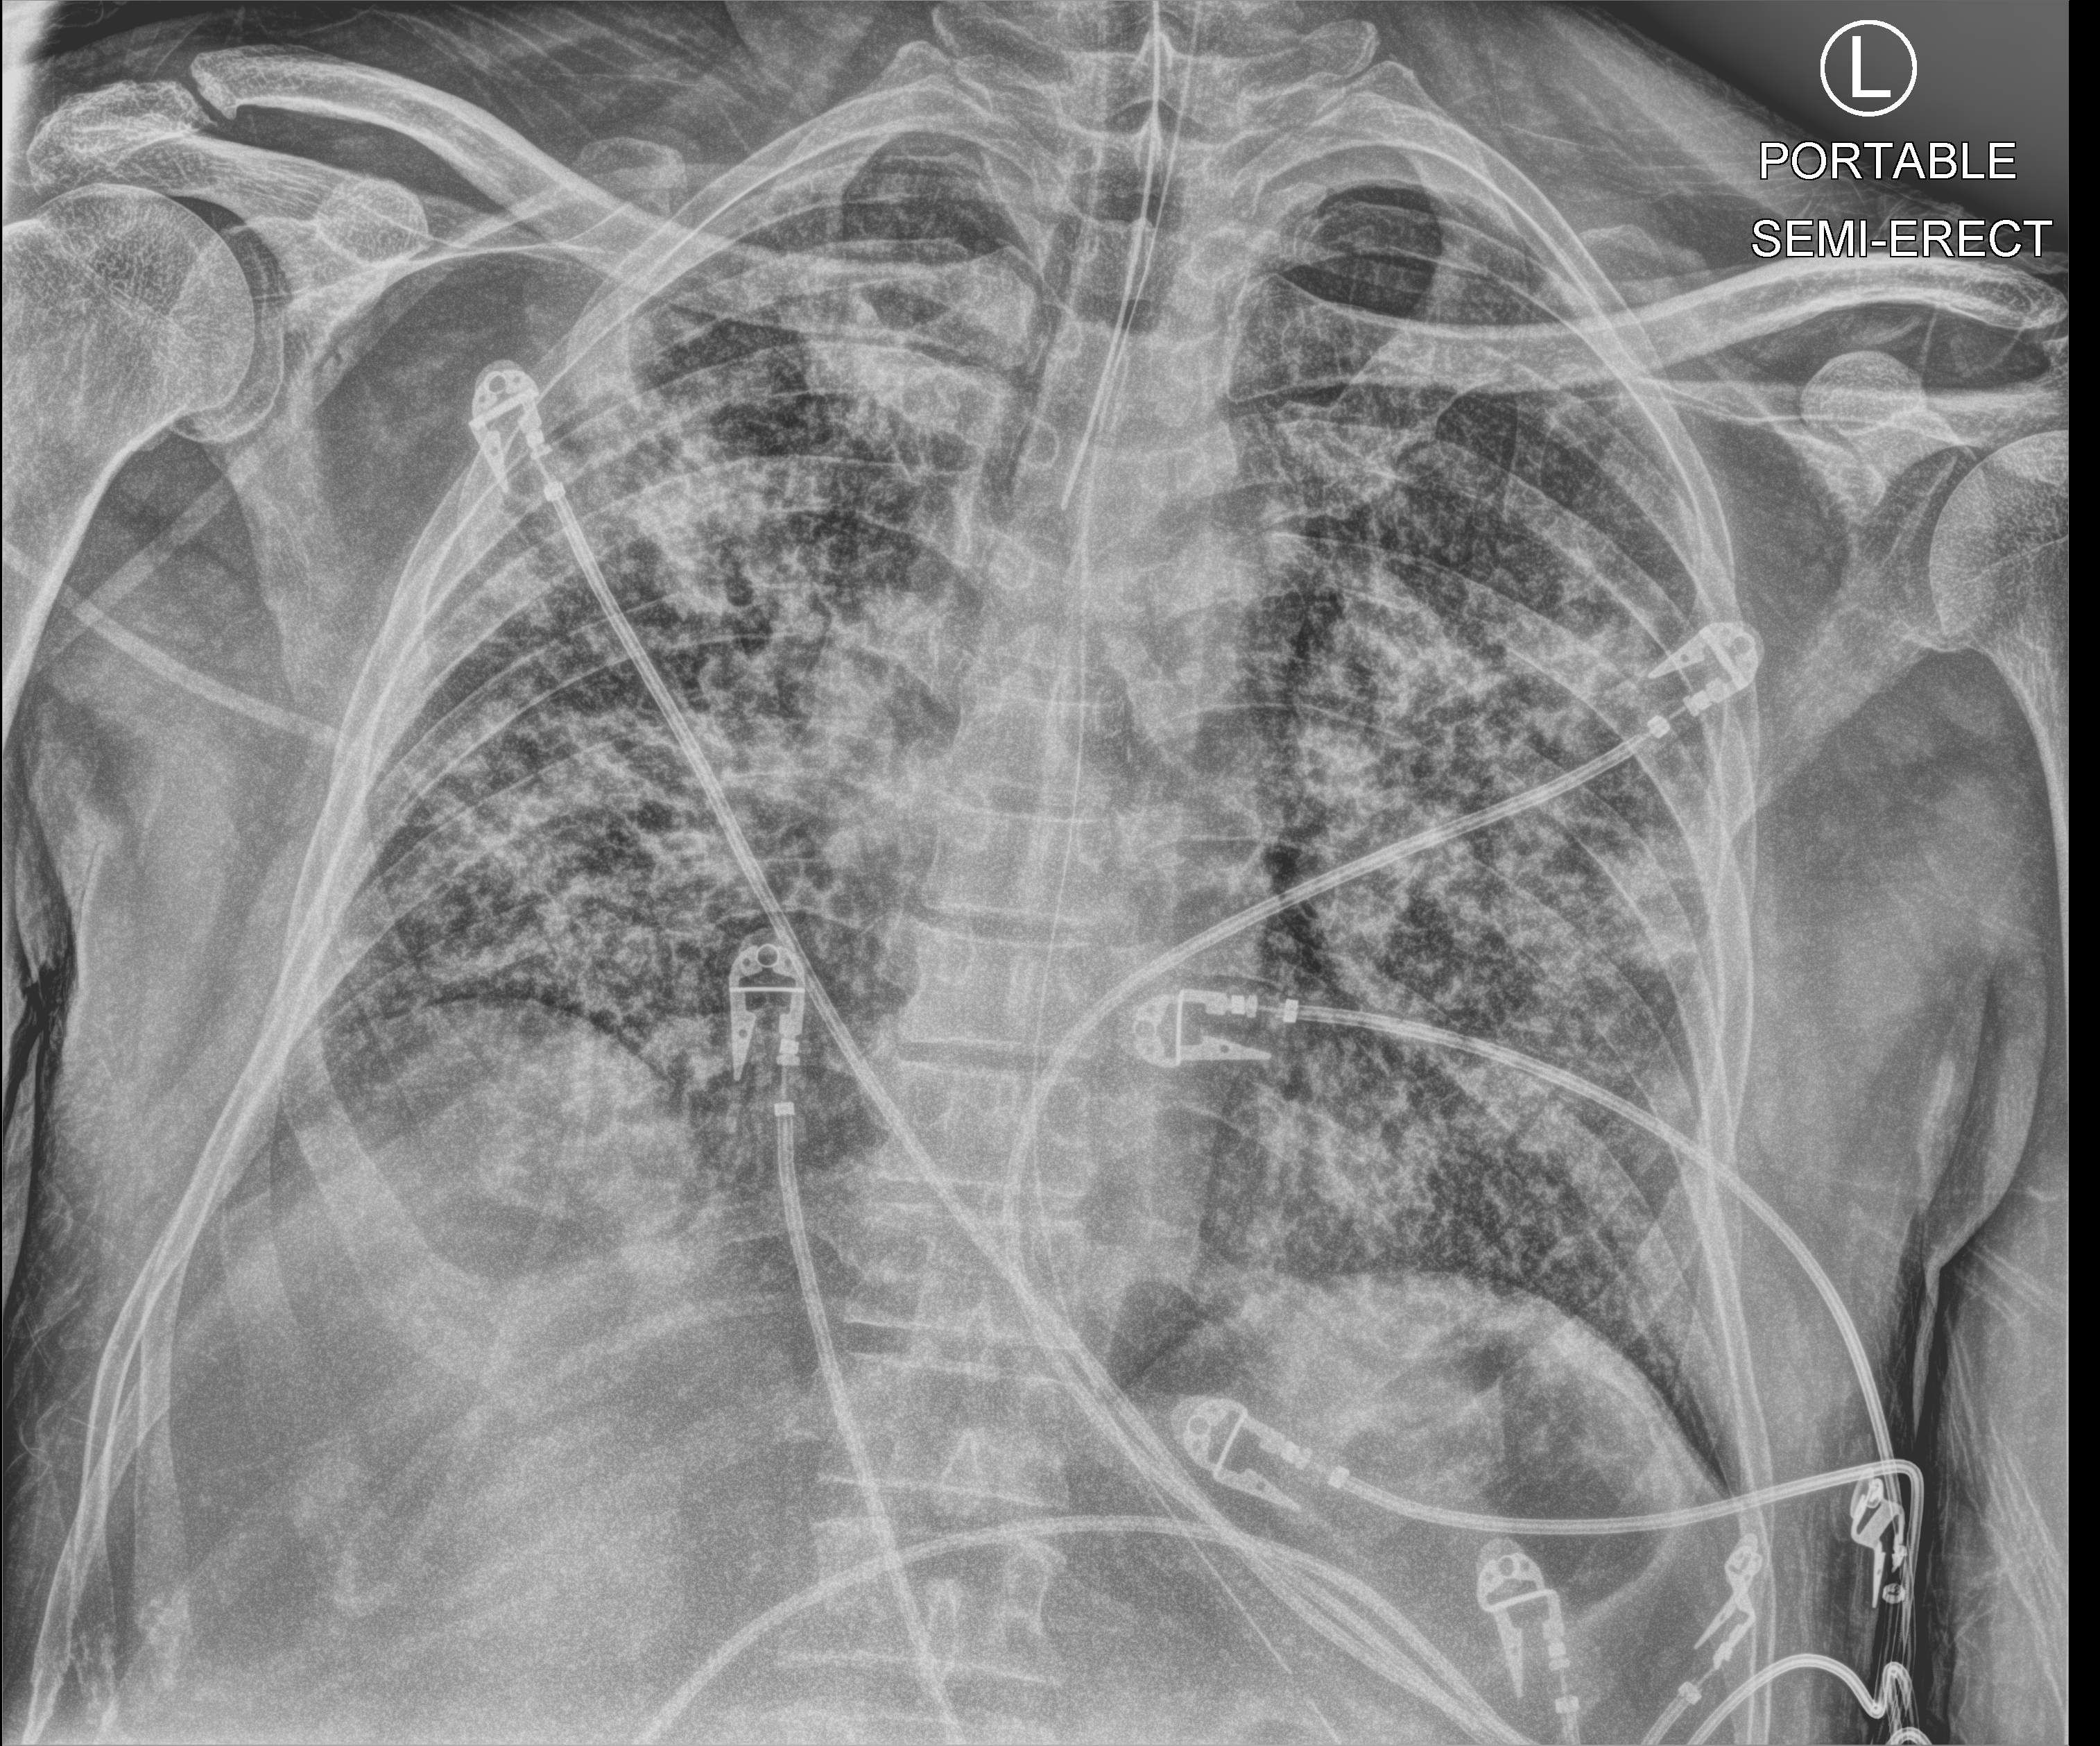
Bedside chest radiograph (computed radiography), anteroposterior (AP) projection. Male patient hospitalised with COVID-19, age 60–74 years.
Admission-level facts for this patient (not findings on this image; timing relative to this image not recorded): admitted to intensive care during this hospital stay: yes.